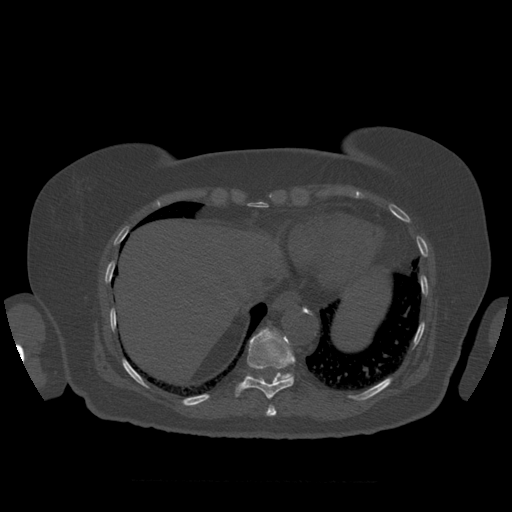
CT including the spine, one axial slice. Reconstruction kernel STANDARD. 120 kVp. Bone window (W 1800 / L 400 HU). 1.25 mm slice thickness. 512 × 512 image matrix. Patient age 81 years. From the clinical record (not read from this slice): primary cancer: renal; vertebrae with lytic lesions (as recorded): L1.
Outlined on this slice (semi-automatically segmented with operator editing):
- T10 vertebra: bounding box <236,328,295,399> (left, top, right, bottom; pixels)
- T11 vertebra: <246,373,293,381>
- T9 vertebra: <266,405,277,417>